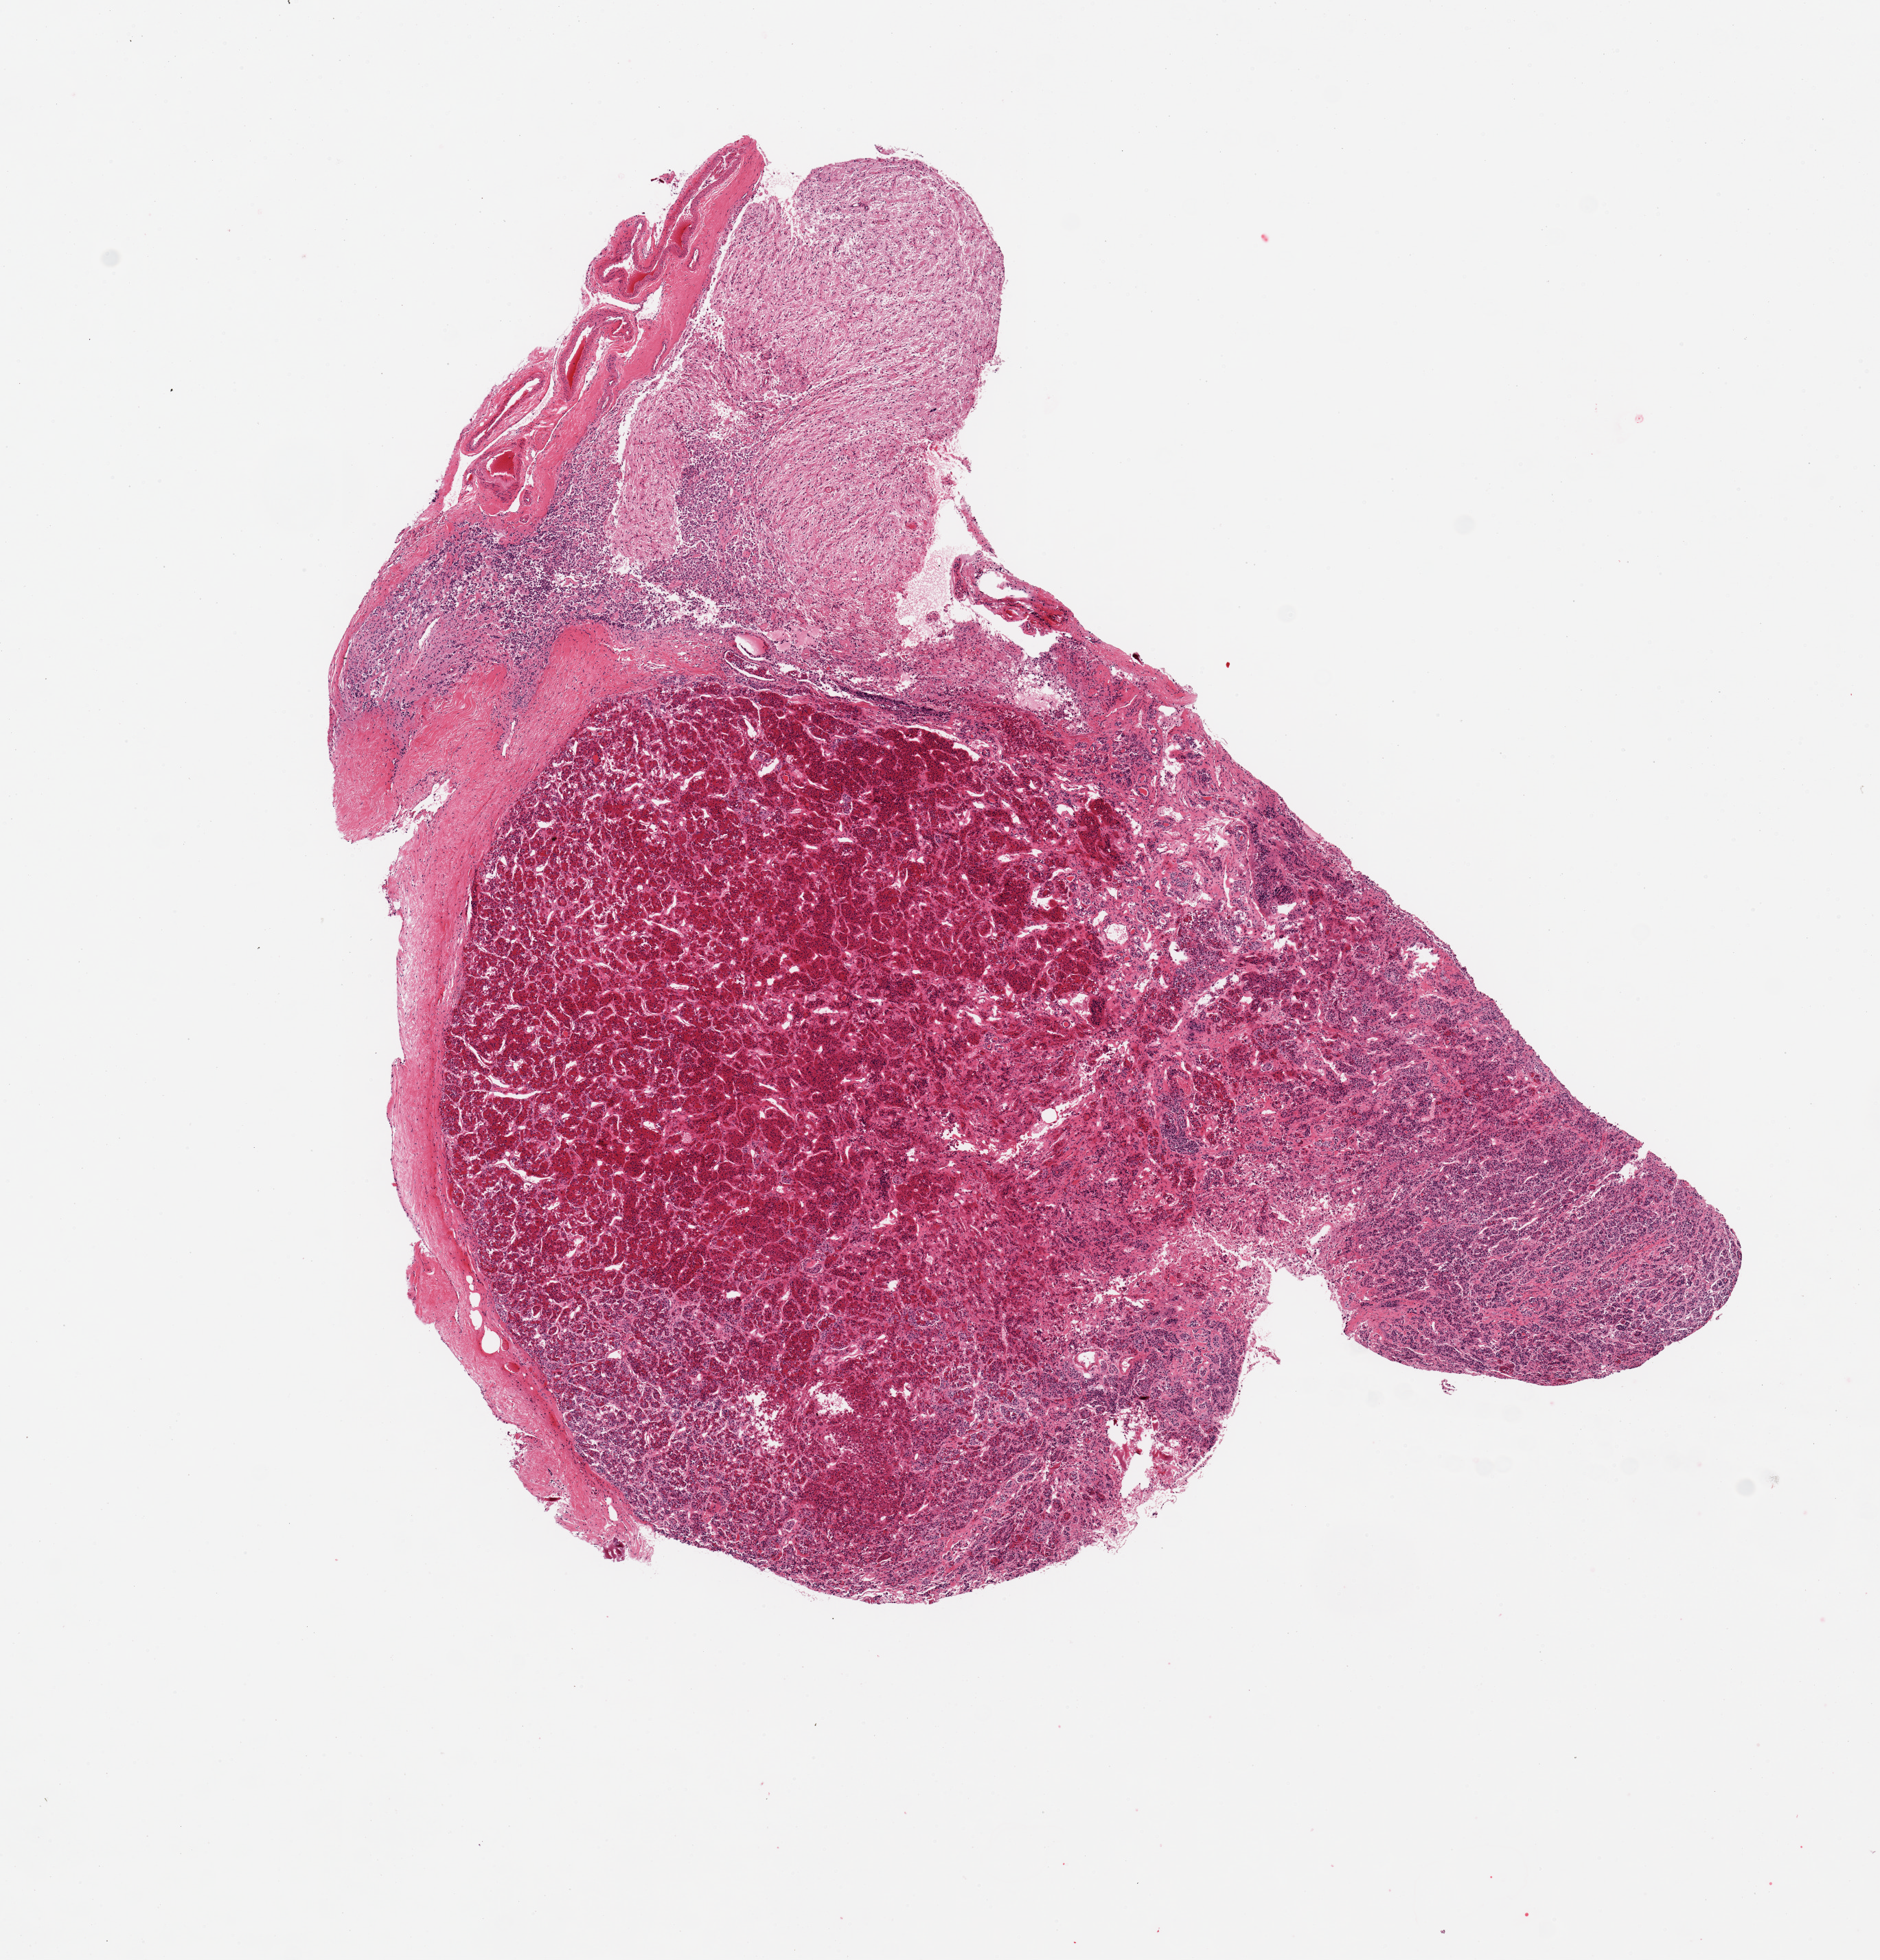
Whole-slide image, haematoxylin and eosin stain, brightfield, whole scanned area (about 10.8 x 11.3 mm, acquisition: 20x scan) shown as a low-resolution overview, PAXgene-fixed, paraffin-embedded tissue, sampled site (target tissue): pituitary, tissue donor sample.
- reviewer comment on this tissue sample: 1 piece: adenohypophysis and neurohypophysis